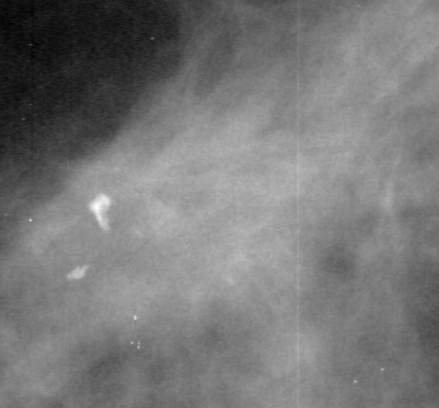
Cropped region of a digitized screen-film mammogram centred on a radiologist-marked abnormality, left breast, CC view.
- Finding: mass, shape irregular, margins spiculated; BI-RADS assessment category 4; pathology (as recorded): malignant.